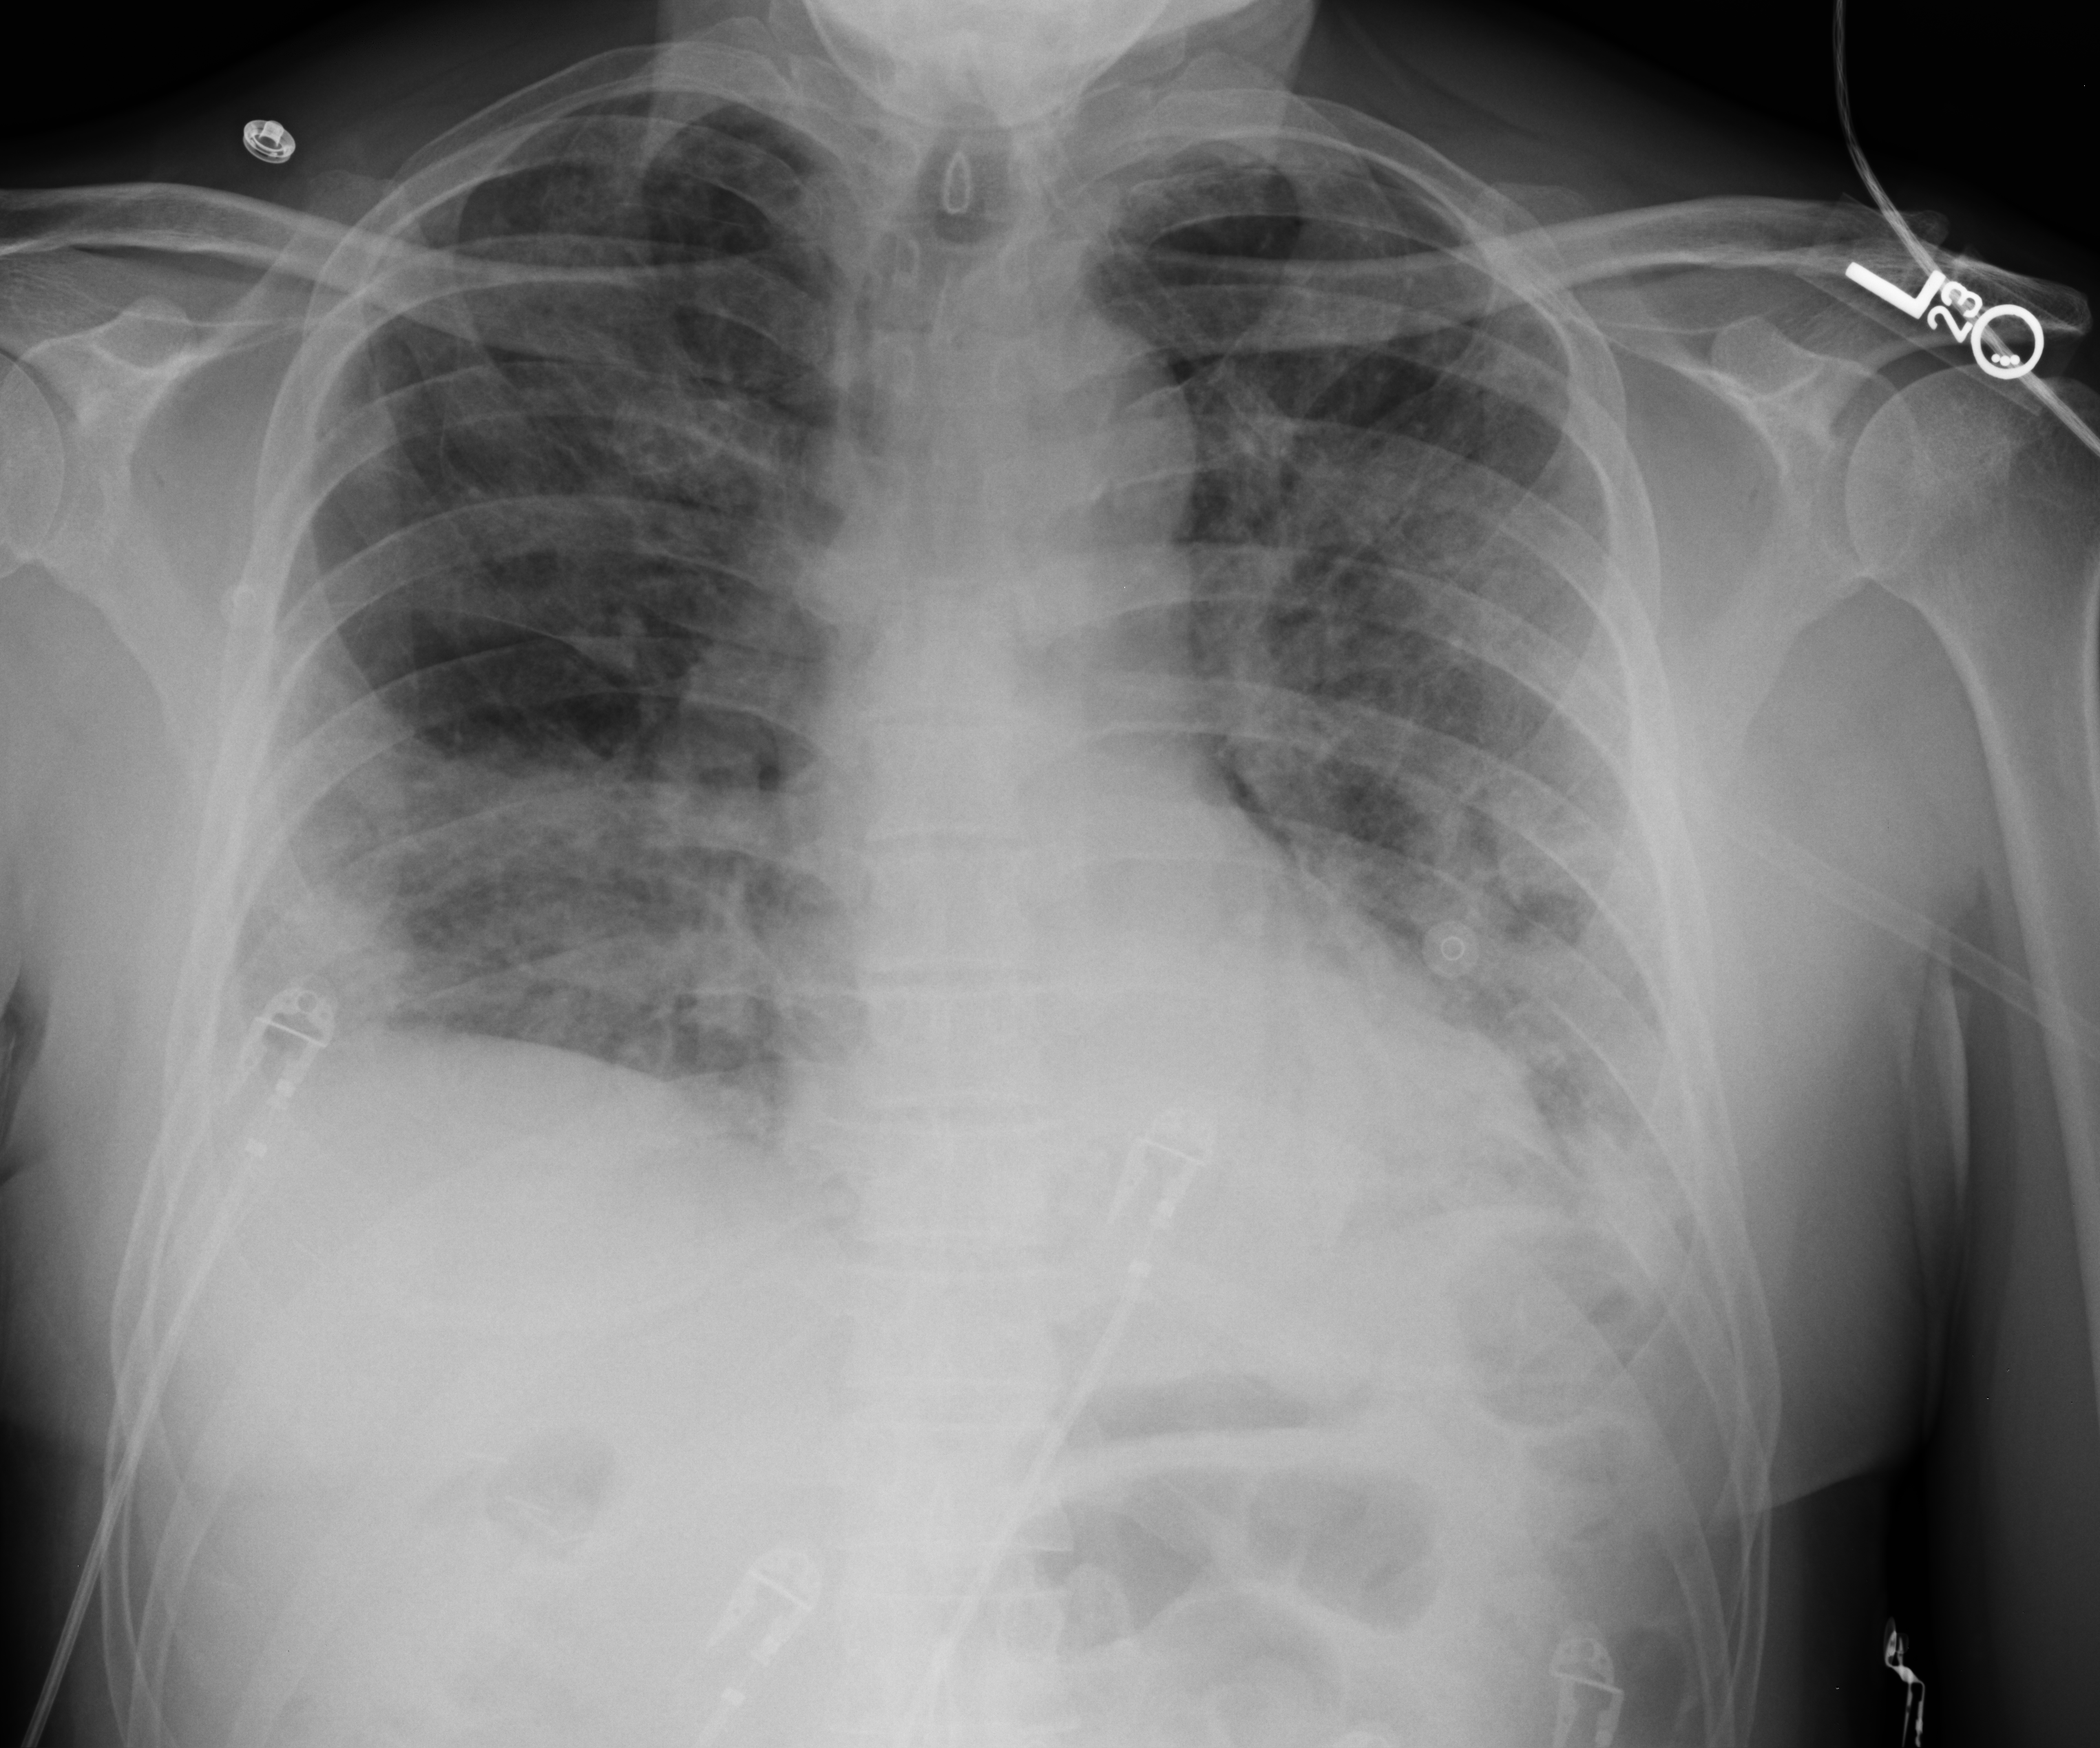
Portable chest radiograph. Male patient hospitalised with COVID-19, age 60–74 years.
Hospital-stay facts (about this admission, not read from this image; timing relative to this image not recorded):
- other chronic lung disease (admission record): no
- mechanically ventilated during this hospital stay: yes